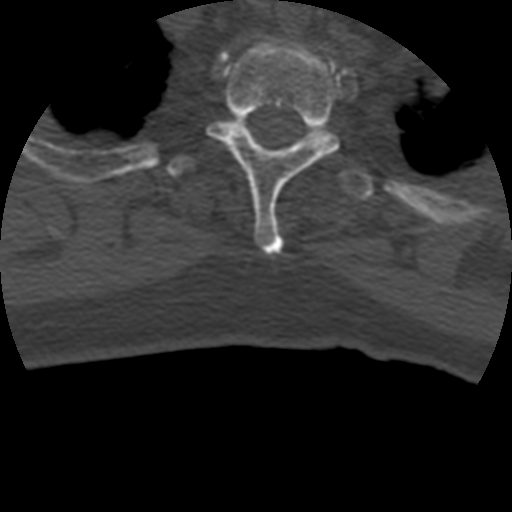
CT including the spine, one axial slice; position 366 of 399 along the scan axis; reconstruction kernel STANDARD; bone window (W 1800 / L 400 HU); 512 × 512 image matrix, field of view 160 × 160 mm. Patient age 69 years. From the clinical record (not read from this slice): primary cancer: prostate.
Structures marked on this image (semi-automatic segmentation, software-assisted and operator-edited):
- T2 vertebra: bounding box [x1, y1, x2, y2] px = [207, 38, 344, 256]
- T3 vertebra: [167, 121, 374, 201]